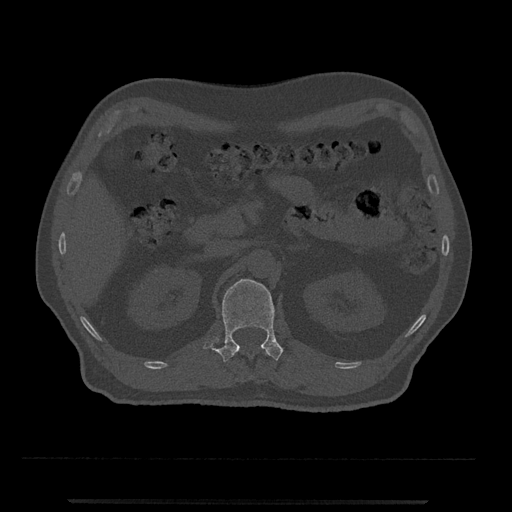
CT including the spine, one axial slice. Slice 350 of 797 in the series (ordered by position). Bone window (W 1800 / L 400 HU). 512 × 512 image matrix, field of view 419 × 419 mm. Patient: male, 63 years. Case-level facts recorded for this patient, not image findings: primary cancer: prostate.
Structures marked on this image (semi-automatic segmentation, software-assisted and operator-edited):
- L1 vertebra: bounding box [x1, y1, x2, y2] px = [203, 279, 283, 364]
- T12 vertebra: [265, 351, 268, 356]